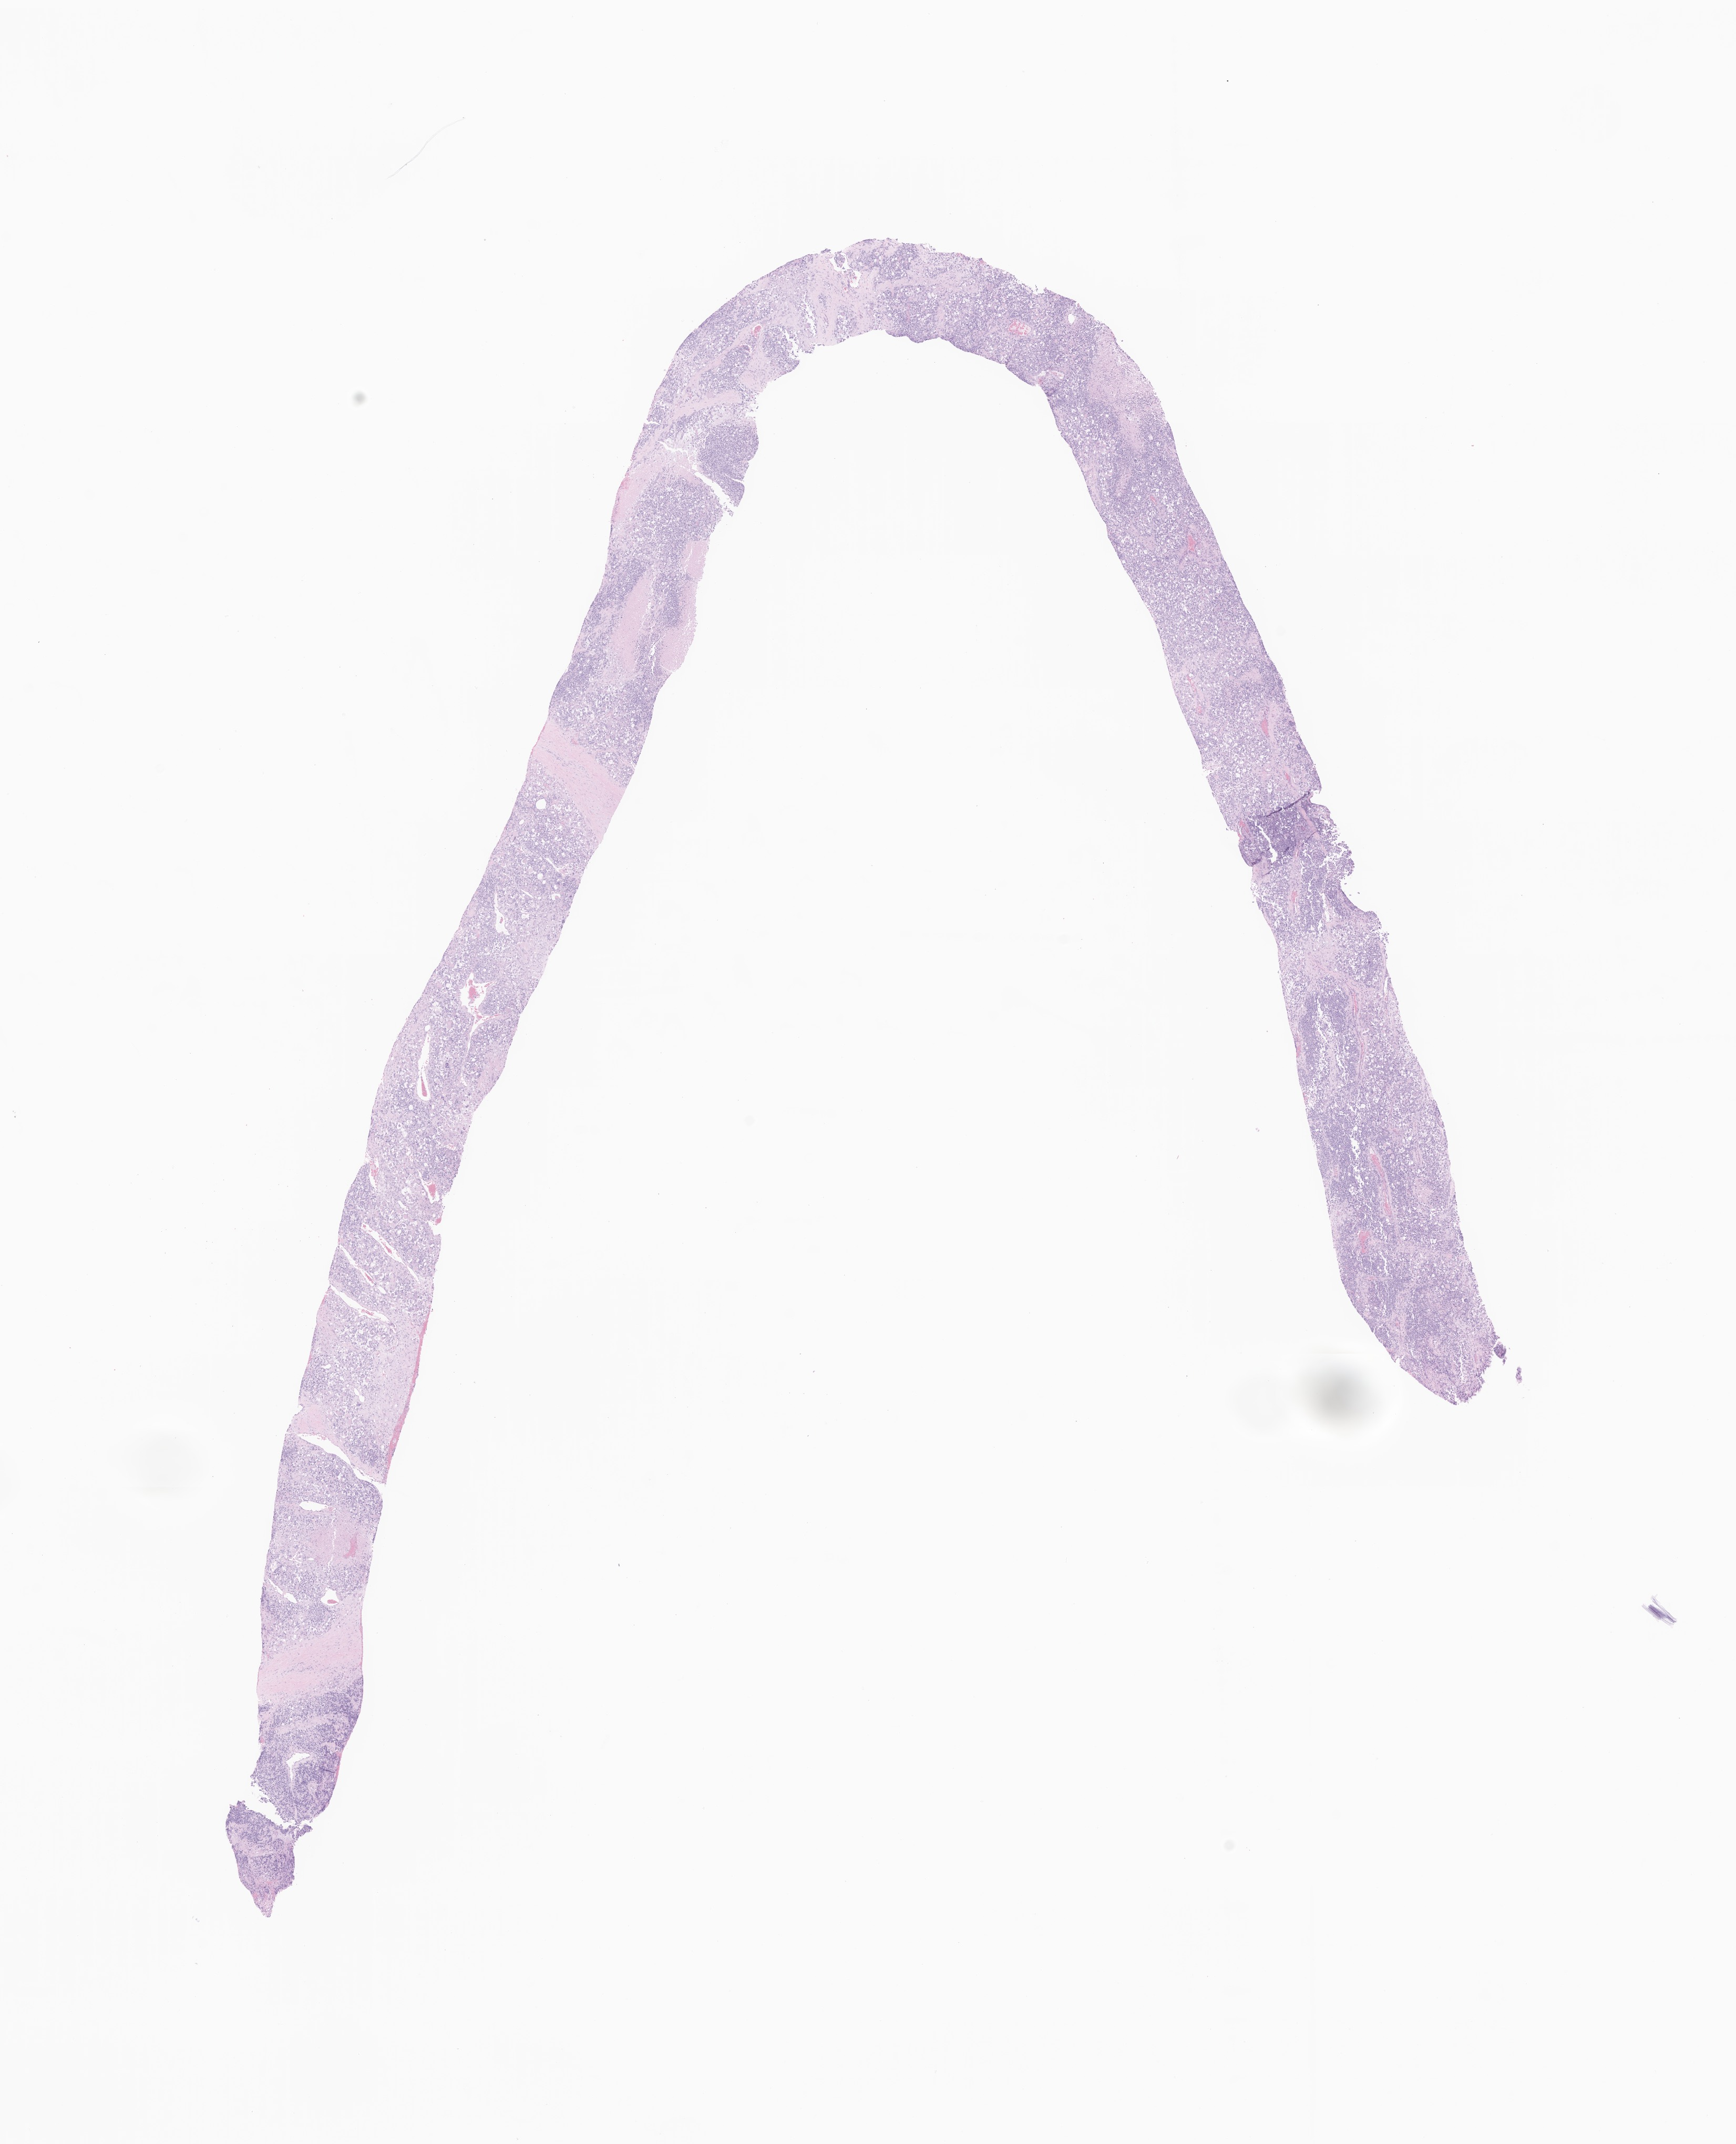
Digitized hematoxylin and eosin (H&E)-stained section of tumor tissue from the pelvis, low-resolution overview of the scanned area, about 13.9 x 17.2 mm. Formalin-fixed, paraffin-embedded (FFPE) tissue. Male patient, age 118 months.
* recorded diagnosis: Embryonal rhabdomyosarcoma, NOS